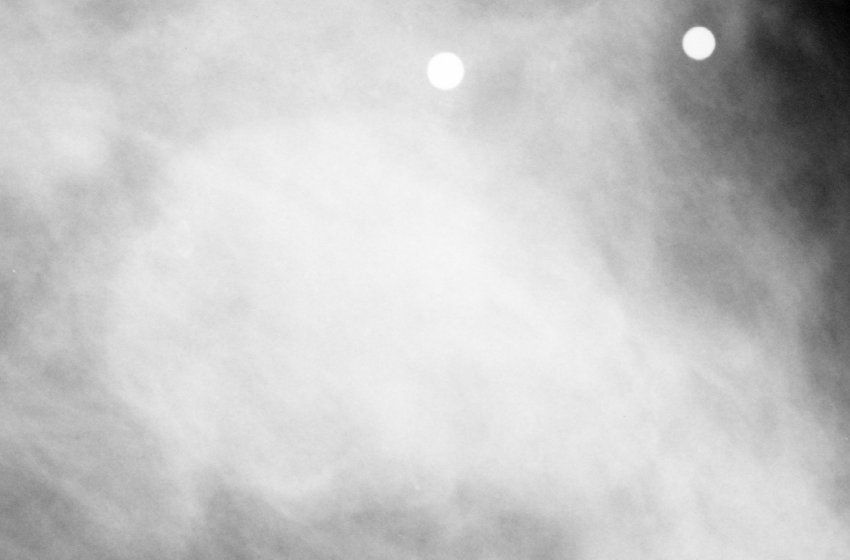
Region of interest cut from a scanned film mammogram (one marked finding), left breast, MLO view.
- Finding: mass, shape irregular, margins spiculated; BI-RADS assessment category 5; pathology (as recorded): malignant.